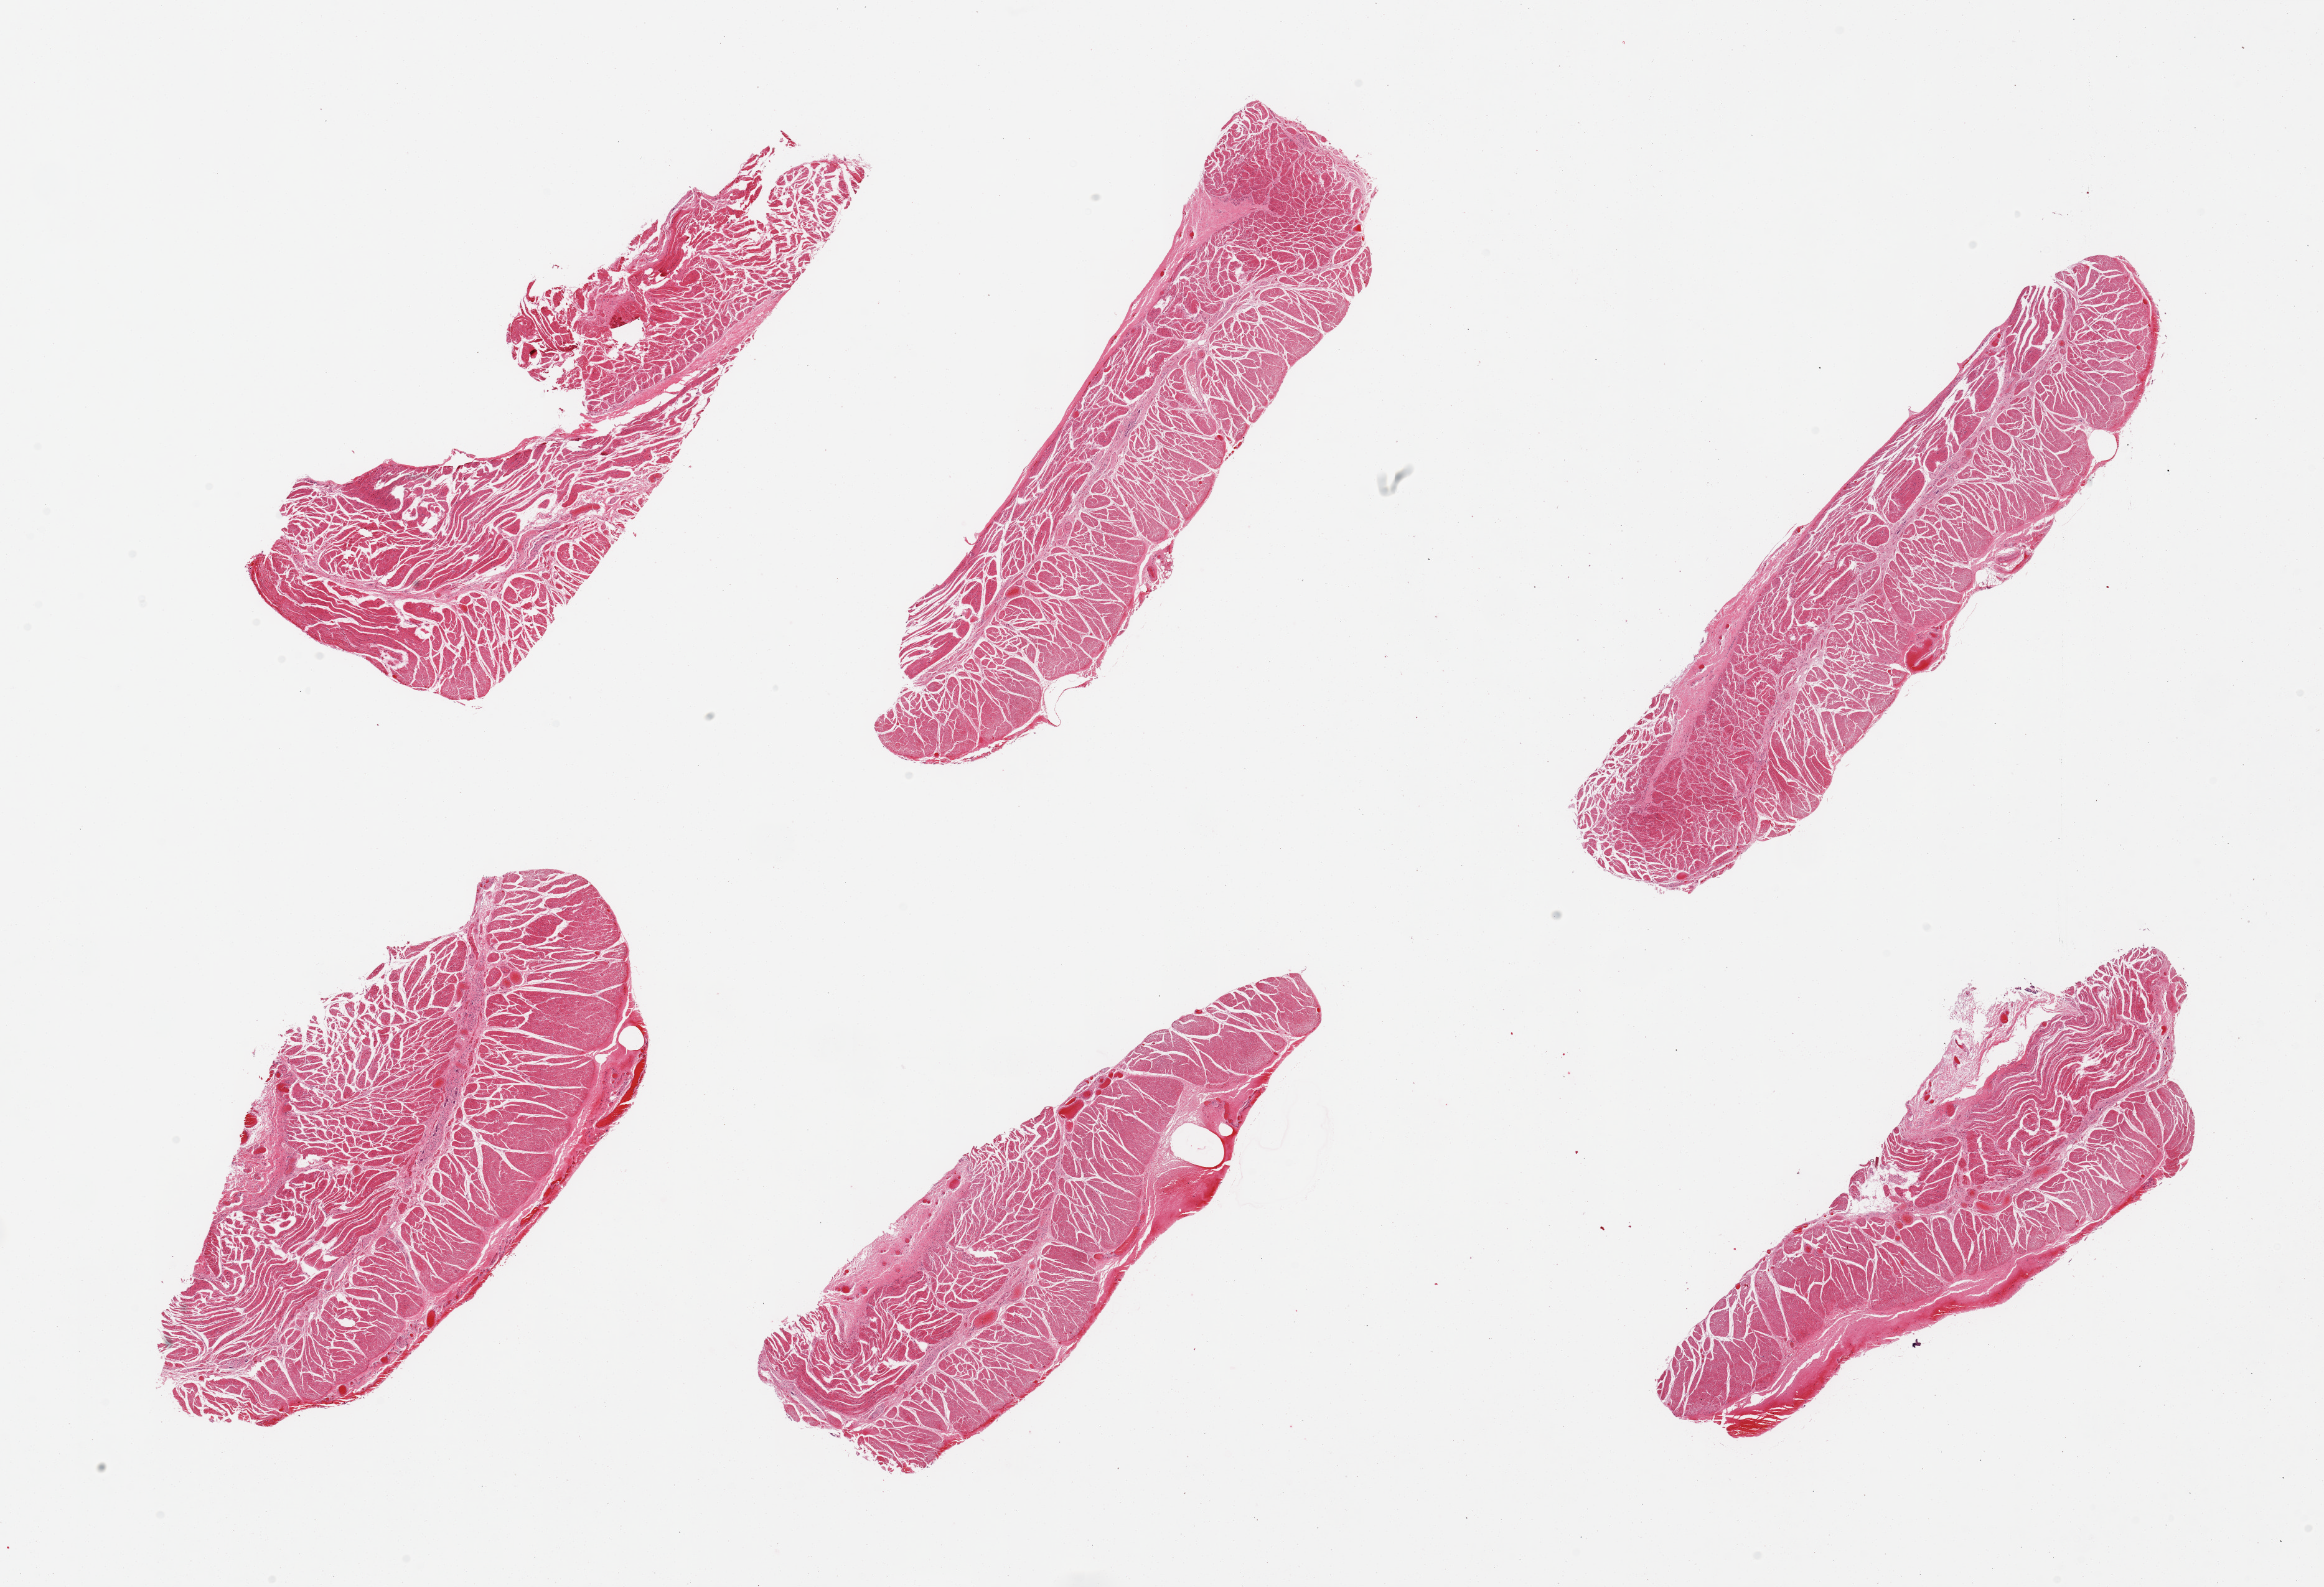
H&E whole-slide image, low-resolution overview of the scanned area, about 29.5 x 20.2 mm, PAXgene-fixed paraffin-embedded (PFPE) section, section of esophageal muscle (target tissue), donor tissue sample. Donor sex: male.
Pathologist's review note for this sample: 6 pieces, all target muscularis, good specimens.